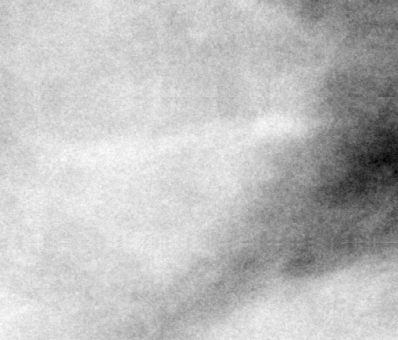
Cropped region of a digitized screen-film mammogram centred on a radiologist-marked abnormality, right breast, MLO view, BI-RADS breast density category 3 (scale 1–4).
- Mass, shape oval, margins obscured; BI-RADS assessment category 3; pathology result (as recorded, not read from the image): benign.